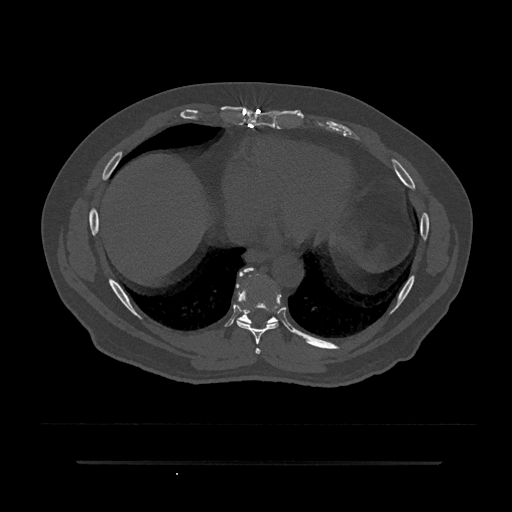
CT including the spine, one axial slice; slice 409 of 797 in the series (ordered by position); 120 kVp; bone window (W 1800 / L 400 HU); 512 × 512 image matrix, field of view 464 × 464 mm. Male patient, age 59 years. Case-level facts recorded for this patient, not image findings: primary cancer: bile ducts; vertebrae with lytic lesions (as recorded): T10.
Outlined on this slice (semi-automatic segmentation, software-assisted and operator-edited):
- T7 vertebra: box from (x=255, y=348) to (x=261, y=354) px
- T8 vertebra: (x=236, y=268)–(x=281, y=345)
- T9 vertebra: (x=237, y=268)–(x=280, y=325)